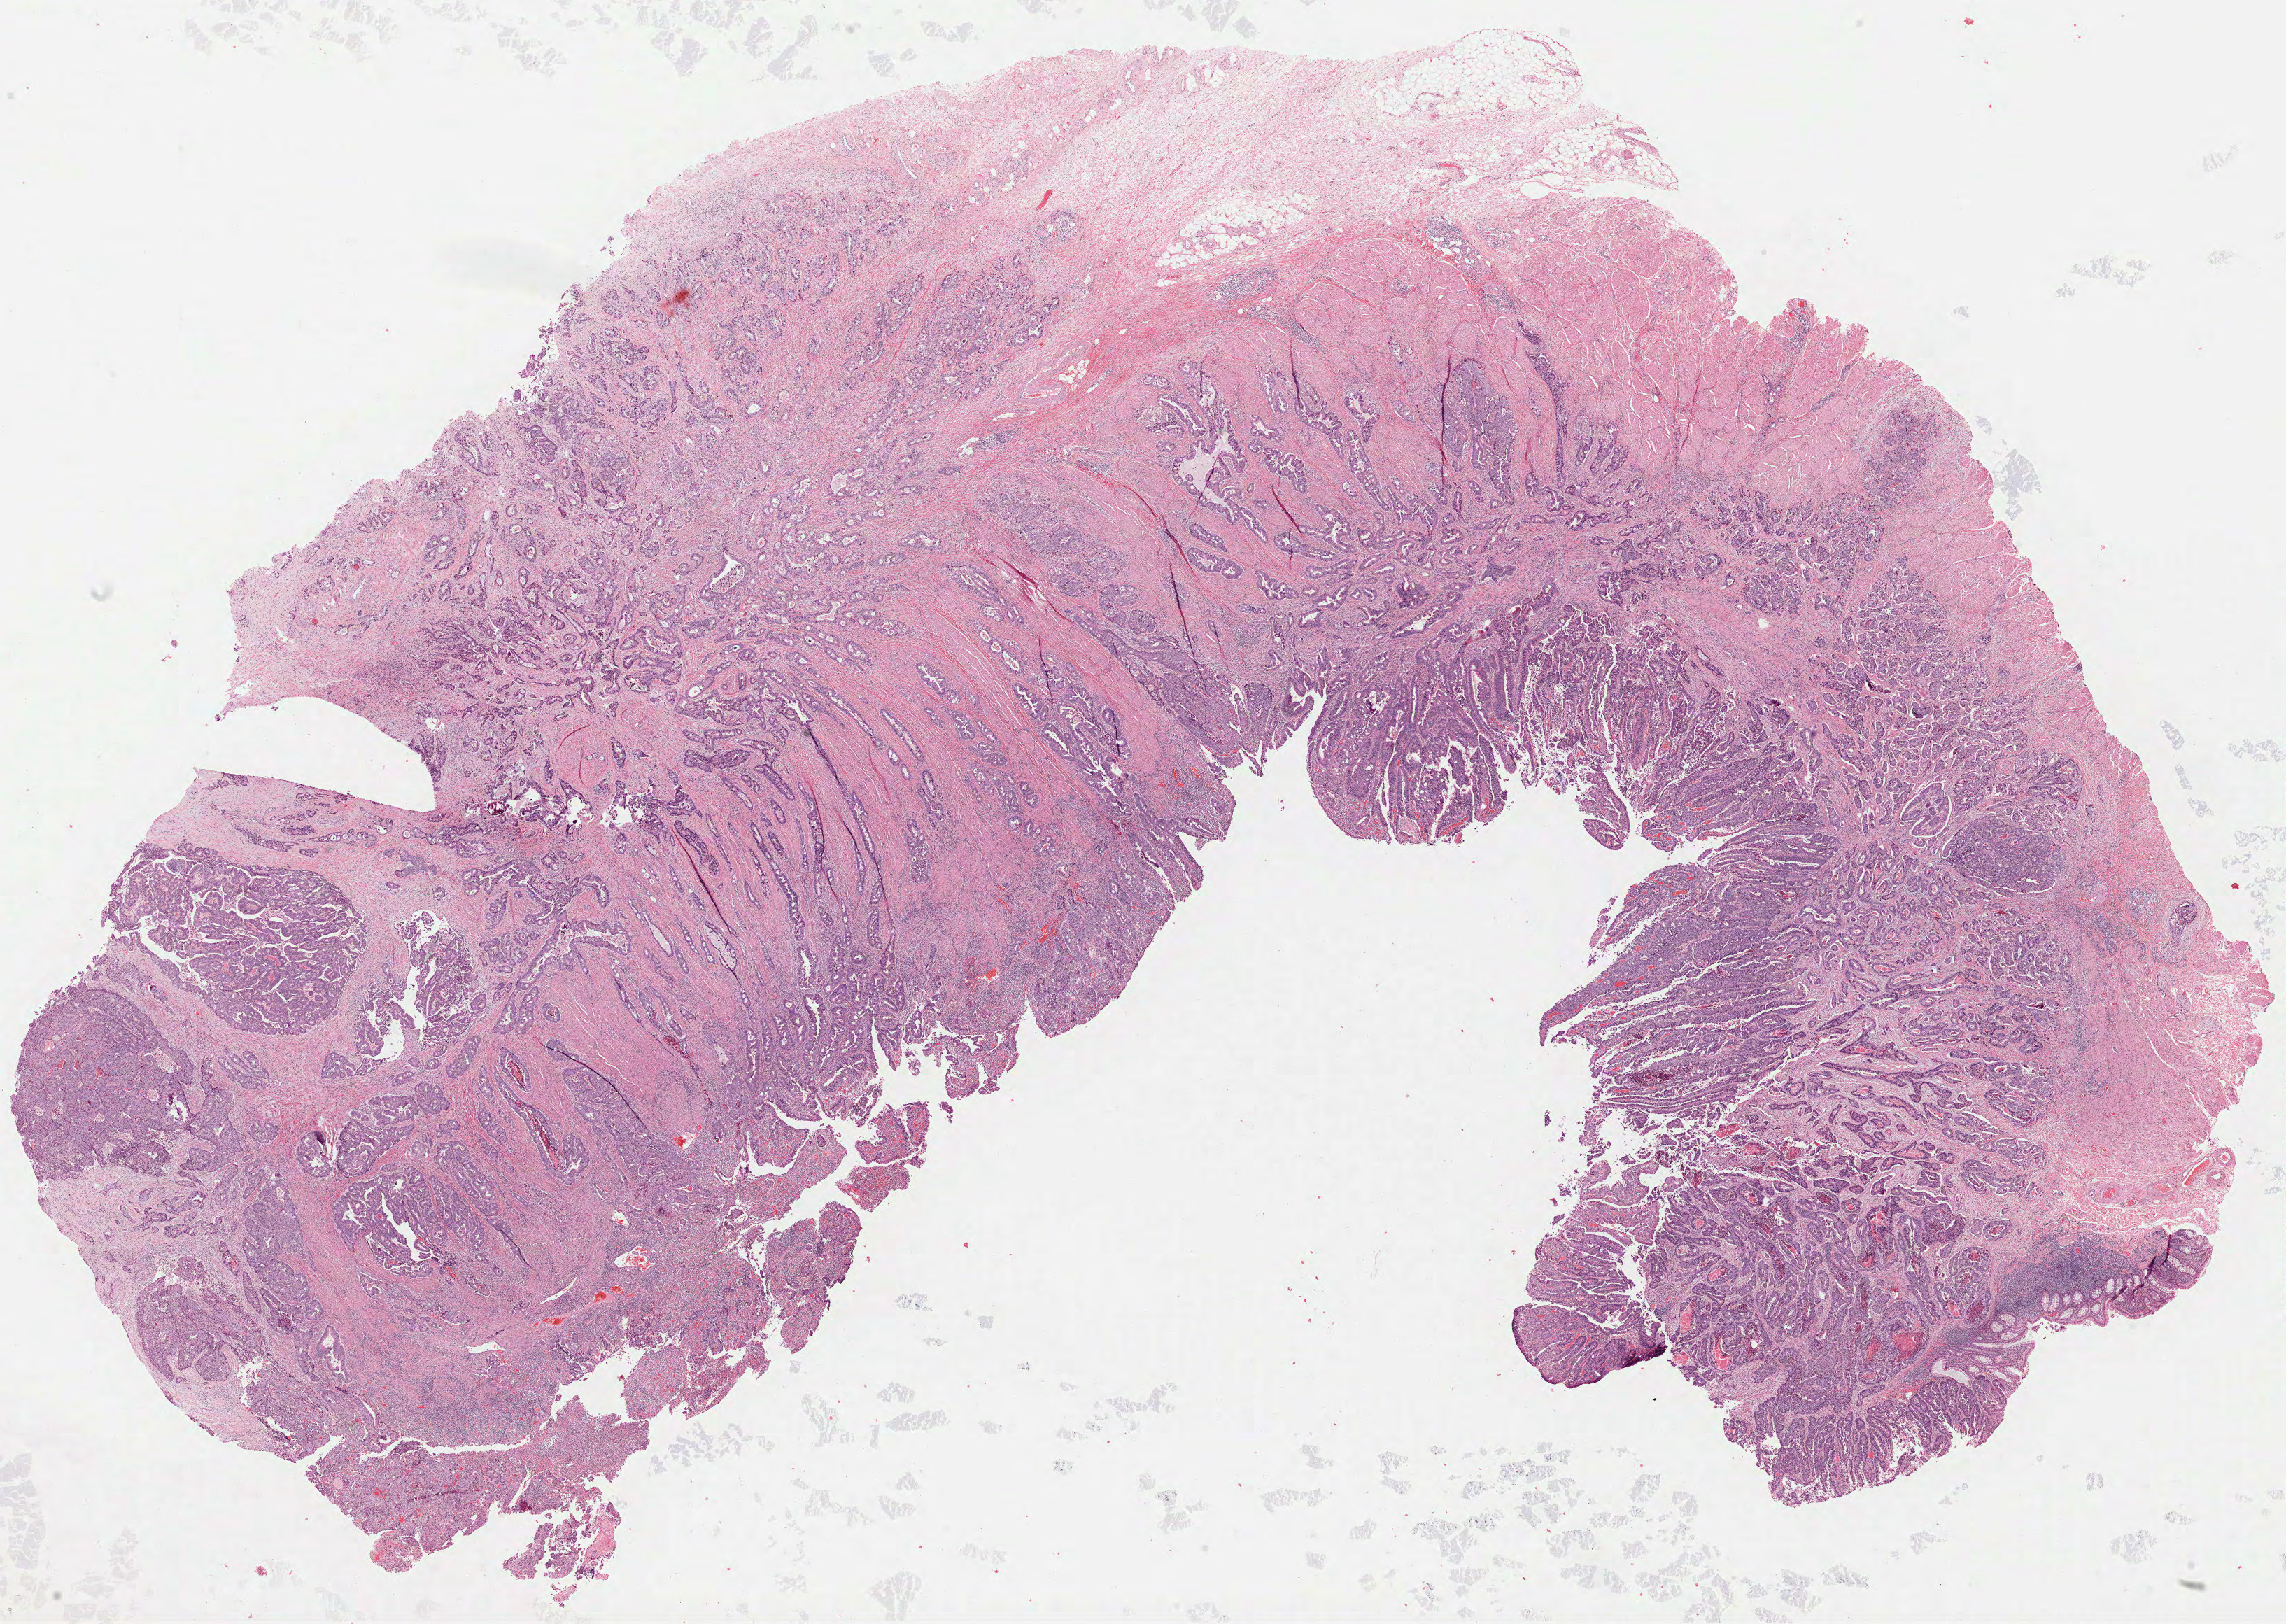
Digitized H&E-stained tissue section (whole slide), a low-resolution overview of the entire scanned area, about 26.3 x 18.7 mm (acquisition: 40x scan). Formalin-fixed paraffin-embedded (FFPE) diagnostic section. Rectum, primary tumour sample. Patient: female, age at initial diagnosis 62 years.
AJCC pathologic stage: IIA (7th edition). Lymph nodes positive (case pathology): 0 of 2 examined. TNM: T3 N0 M0. Pathologic diagnosis: Adenocarcinoma, NOS.